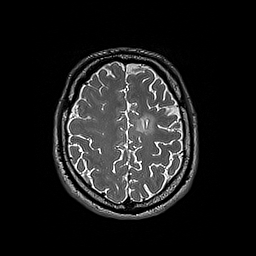
Brain MRI from a brain-tumour surgery series, one axial slice; 1 mm slice thickness; 256 × 256 image matrix. Case-level facts recorded for this patient, not image findings: histopathology: Oligodendroglioma; WHO grade: 3.
Structures marked on this image (manually delineated by an expert):
- tumour: bounding box <136,115,157,135> (left, top, right, bottom; pixels)